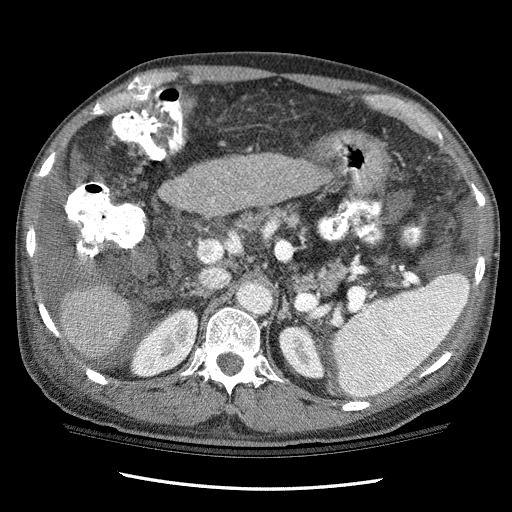
Contrast-enhanced abdominal CT (liver protocol), one axial slice; reconstruction kernel STANDARD; 120 kVp; one of 3 acquisitions stored at this slice position; soft-tissue window (W 400 / L 40 HU); 2.5 mm slice thickness; 512 × 512 image matrix. From the clinical record (not read from this slice): diagnosis: hepatocellular carcinoma (patient treated with transarterial chemoembolisation; whether this scan precedes or follows treatment is not stated here); TNM stage (as recorded): Stage-I; Child-Pugh class: C; tumour differentiation: well differentiated.
Structures marked on this image (semi-automatic segmentation, software-assisted and operator-edited):
- liver parenchyma outside the tumour (the mass and vessels are separate outlines, so this box may not span the whole liver): bounding box <60,153,327,364> (left, top, right, bottom; pixels)